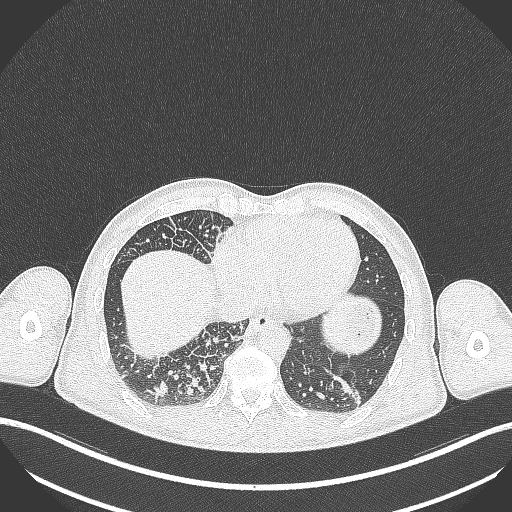
Chest CT, one axial slice. Position 81 of 348 along the scan axis. Reconstruction kernel B70f. Lung window (W 1500 / L -600 HU). 1 mm slice thickness. 512 × 512 image matrix. Patient: male, 49 years. Case-level facts recorded for this patient, not image findings: clinical TNM (as recorded): T2b N1 M0.
Outlined on this slice (bounding box drawn by a radiologist):
- lung tumour (recorded histology: adenocarcinoma): bounding box <333,374,366,408> (left, top, right, bottom; pixels)